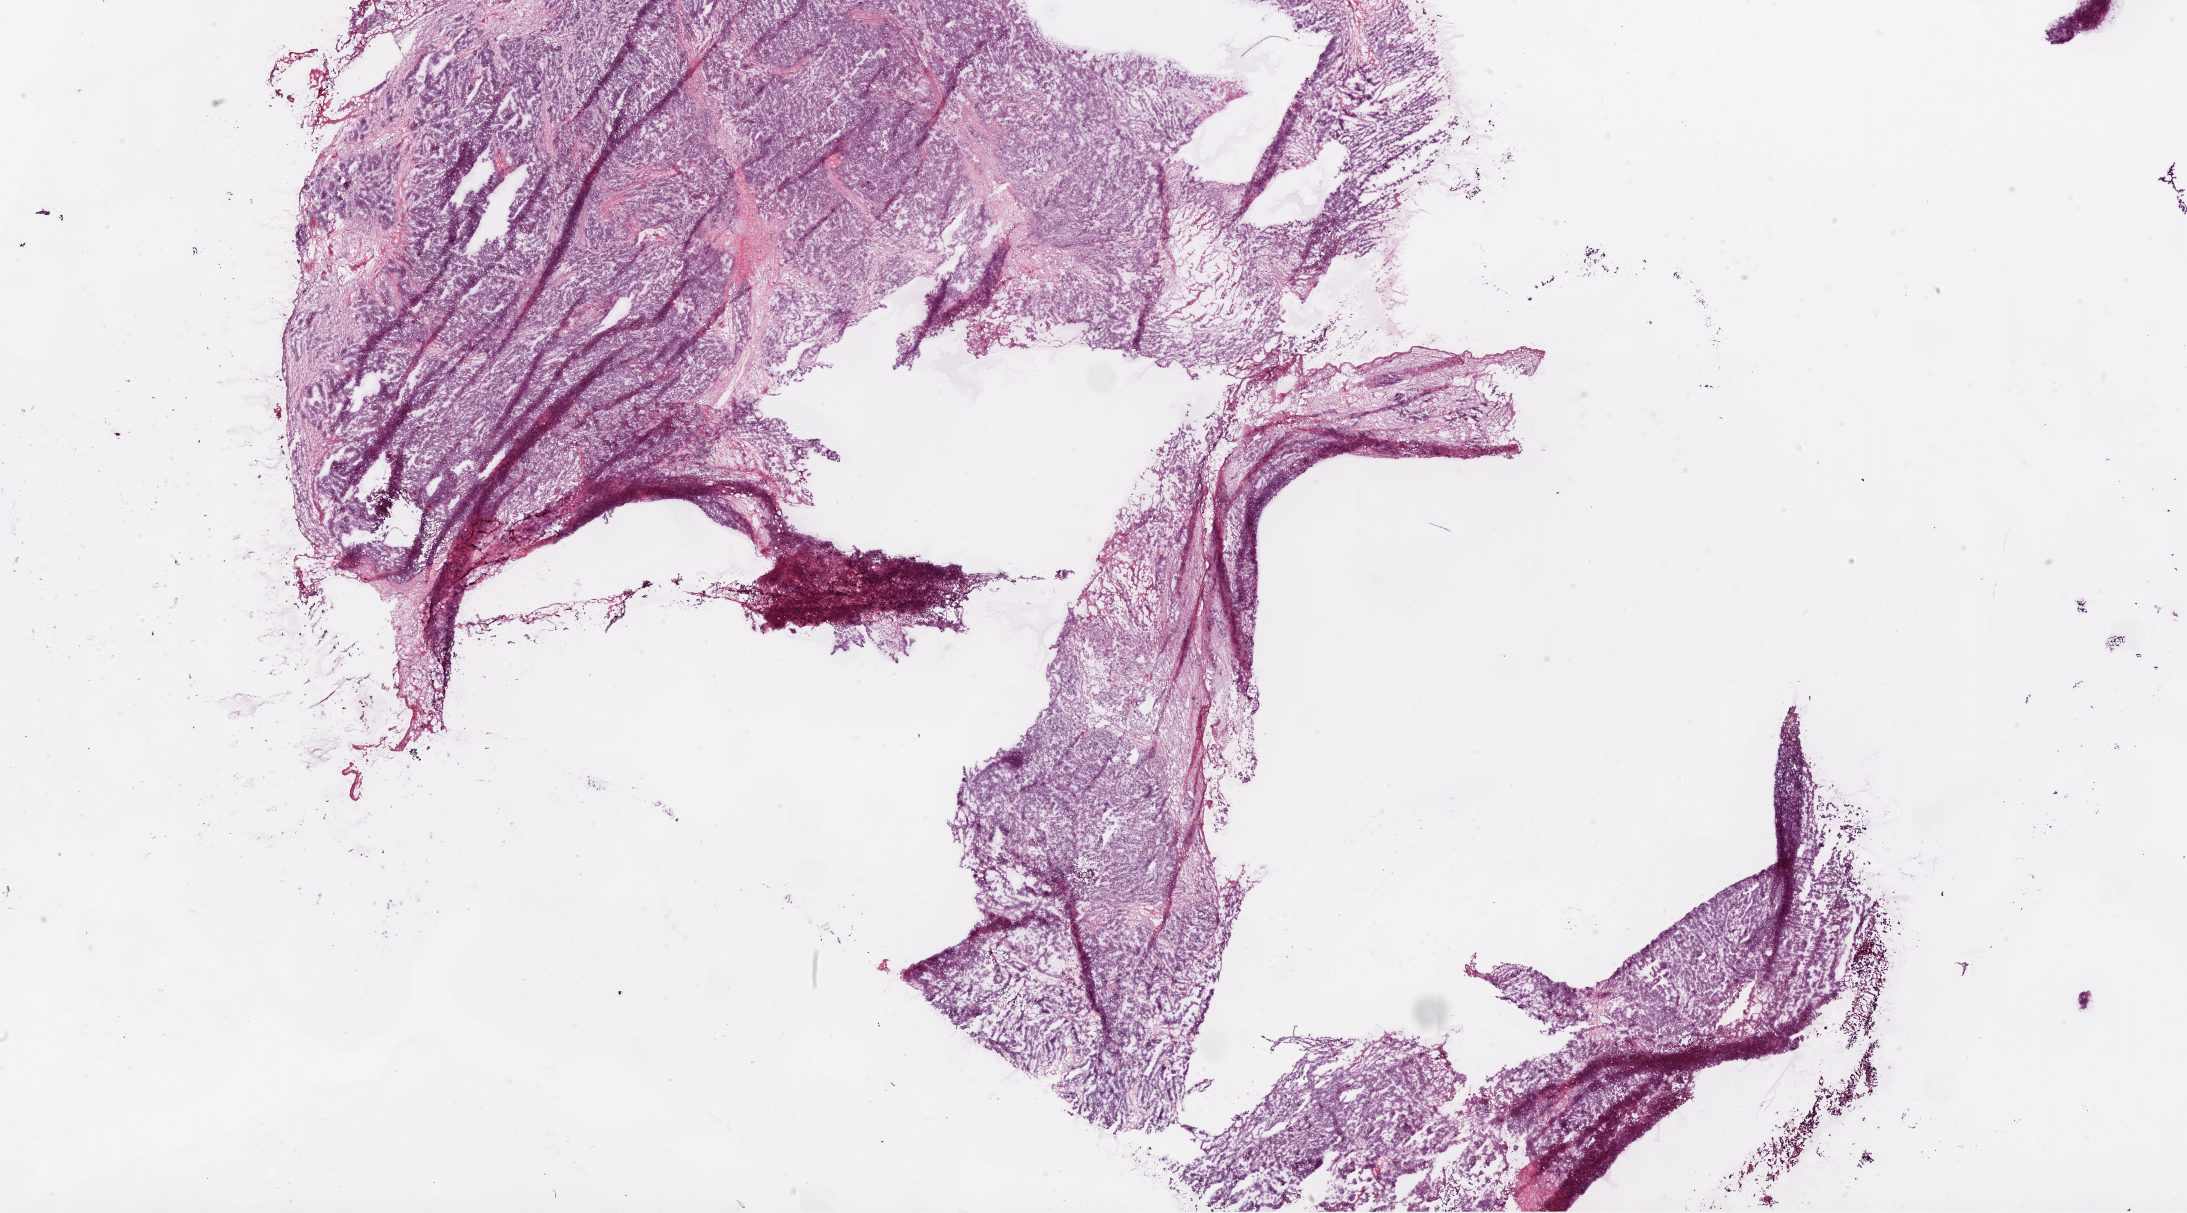
Whole-slide histology image, H&E — whole scanned area (about 35.1 x 19.5 mm) shown as a low-resolution overview, frozen section, primary tumour sample from the ovary. Female, age 63 years at initial diagnosis. Histologic grade: G3 (poorly differentiated). Composition of this section per pathologist review: tumour cells 90%, tumour nuclei 85%, normal cells 0%, stromal cells 10%, necrosis 0%. Inflammatory infiltration, as recorded: lymphocyte infiltration 5%, monocyte infiltration 0%, neutrophil infiltration 0%.
Diagnosis: Serous cystadenocarcinoma, NOS. FIGO stage: IV.